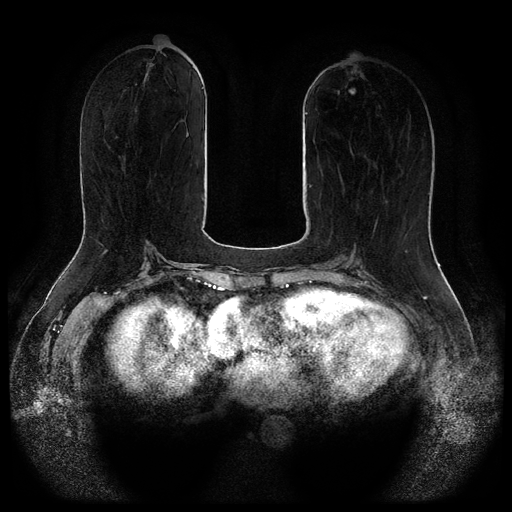
Breast MRI (dynamic contrast-enhanced, multi-phase), one axial slice. Position 34 of 116 along the scan axis. Dynamic contrast-enhanced series, time point 2 of 5 at this slice position (early post-contrast). 1.5 T. TE 2.6 ms, TR 5.3 ms. 2.1 mm slice thickness. 512 × 512 image matrix, field of view 360 × 360 mm. Patient: female, 65 years.
Outlined on this slice (semi-automatic segmentation, software-assisted and operator-edited):
- breast lesion (labelled benign in the annotation): bounding box <349,88,356,95> (left, top, right, bottom; pixels)